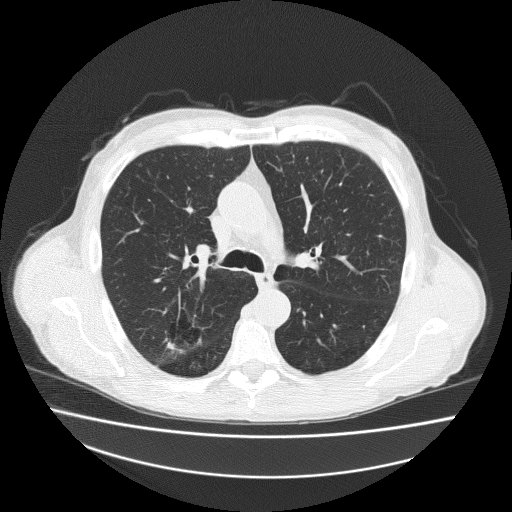
Low-dose screening chest CT, axial slice; second annual screen; lung window (W 1500 / L -600 HU); lung (sharp) reconstruction kernel (FC51); 120 kVp; slice 72 of 186 in the series; 512 × 512 image matrix. Male participant, aged 73 years at enrolment.
• Expert-annotated lung lesion, bounding box [x1, y1, x2, y2] px = [157, 312, 211, 354].
• Screening reader's record for this exam: no non-calcified nodule ≥4 mm recorded.
• Later outcome: lung cancer diagnosed 418 days after this screen — adenosquamous carcinoma, right upper lobe, well differentiated (G1), stage IA (AJCC 6th edition), 20 mm at pathology.